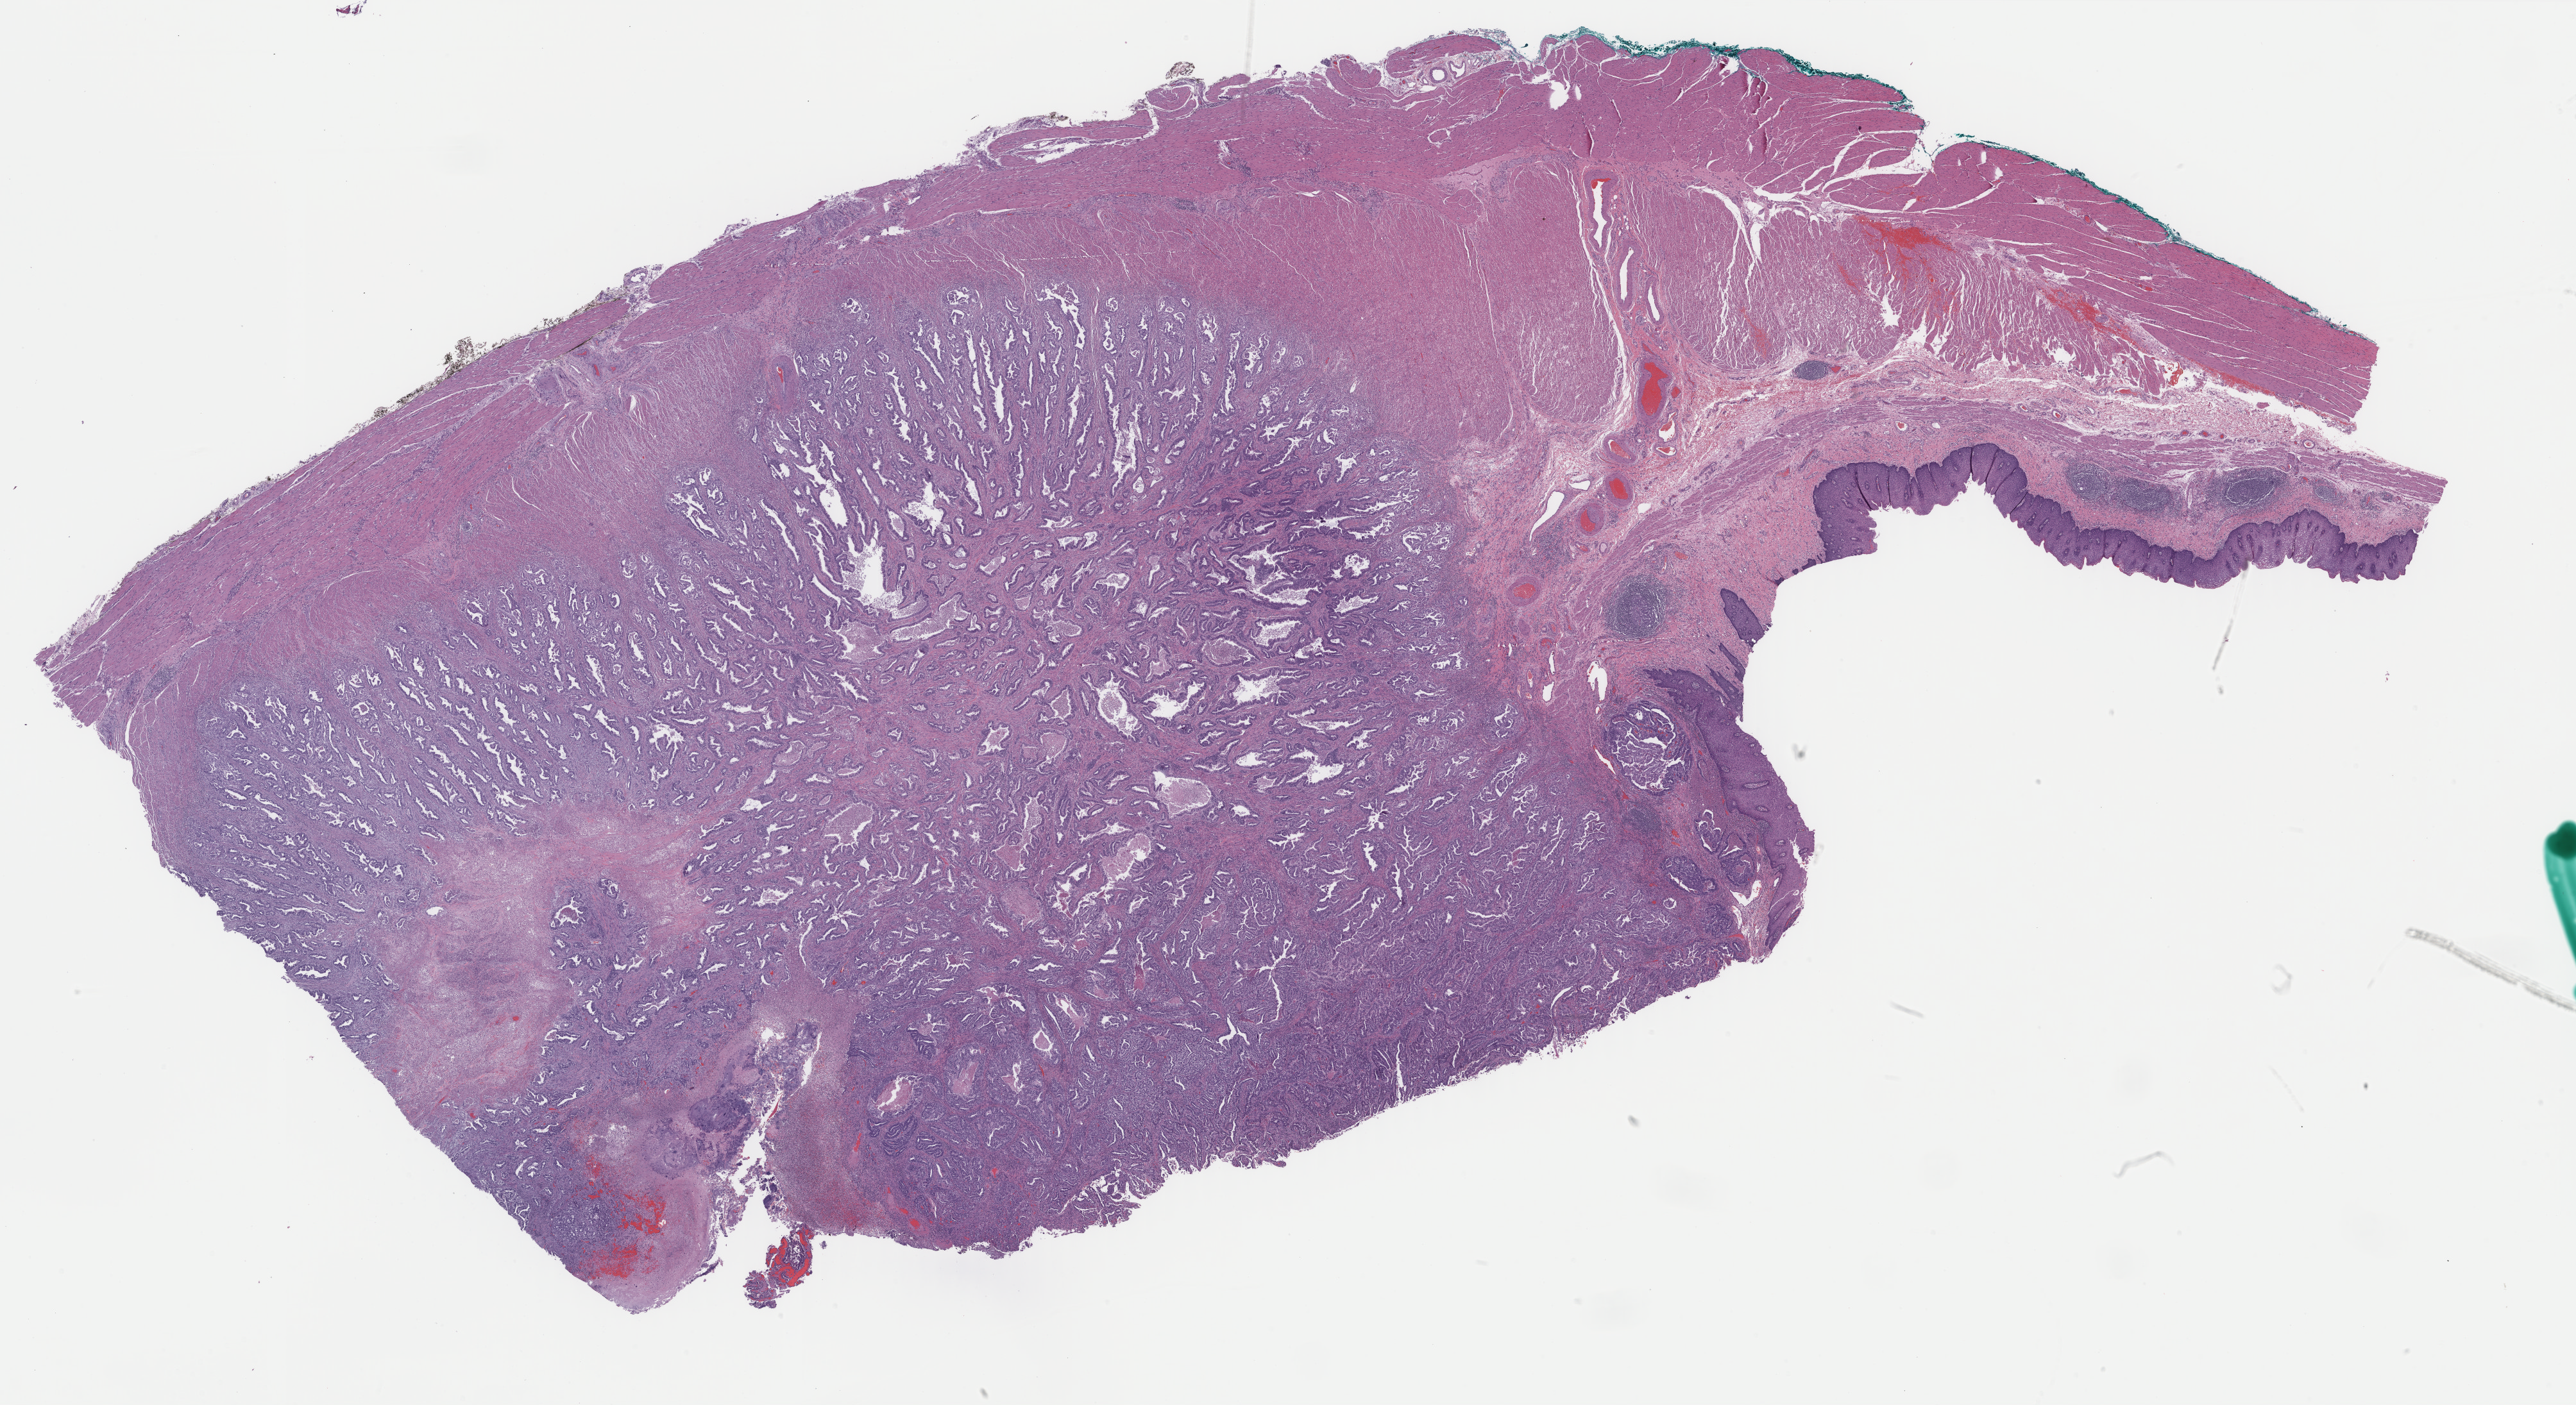
H&E-stained whole-slide image, low-resolution overview of the scanned area, about 31.9 x 17.4 mm; formalin-fixed paraffin-embedded (FFPE) diagnostic section; sample: primary tumour, esophagus. Male patient; age at initial diagnosis 75 years. Histologic grade: GX (grade cannot be assessed).
Pathologic diagnosis: Adenocarcinoma, NOS (lower third of esophagus). Lymph nodes positive (case pathology): 6 of 12 examined. AJCC pathologic stage: IIIA.